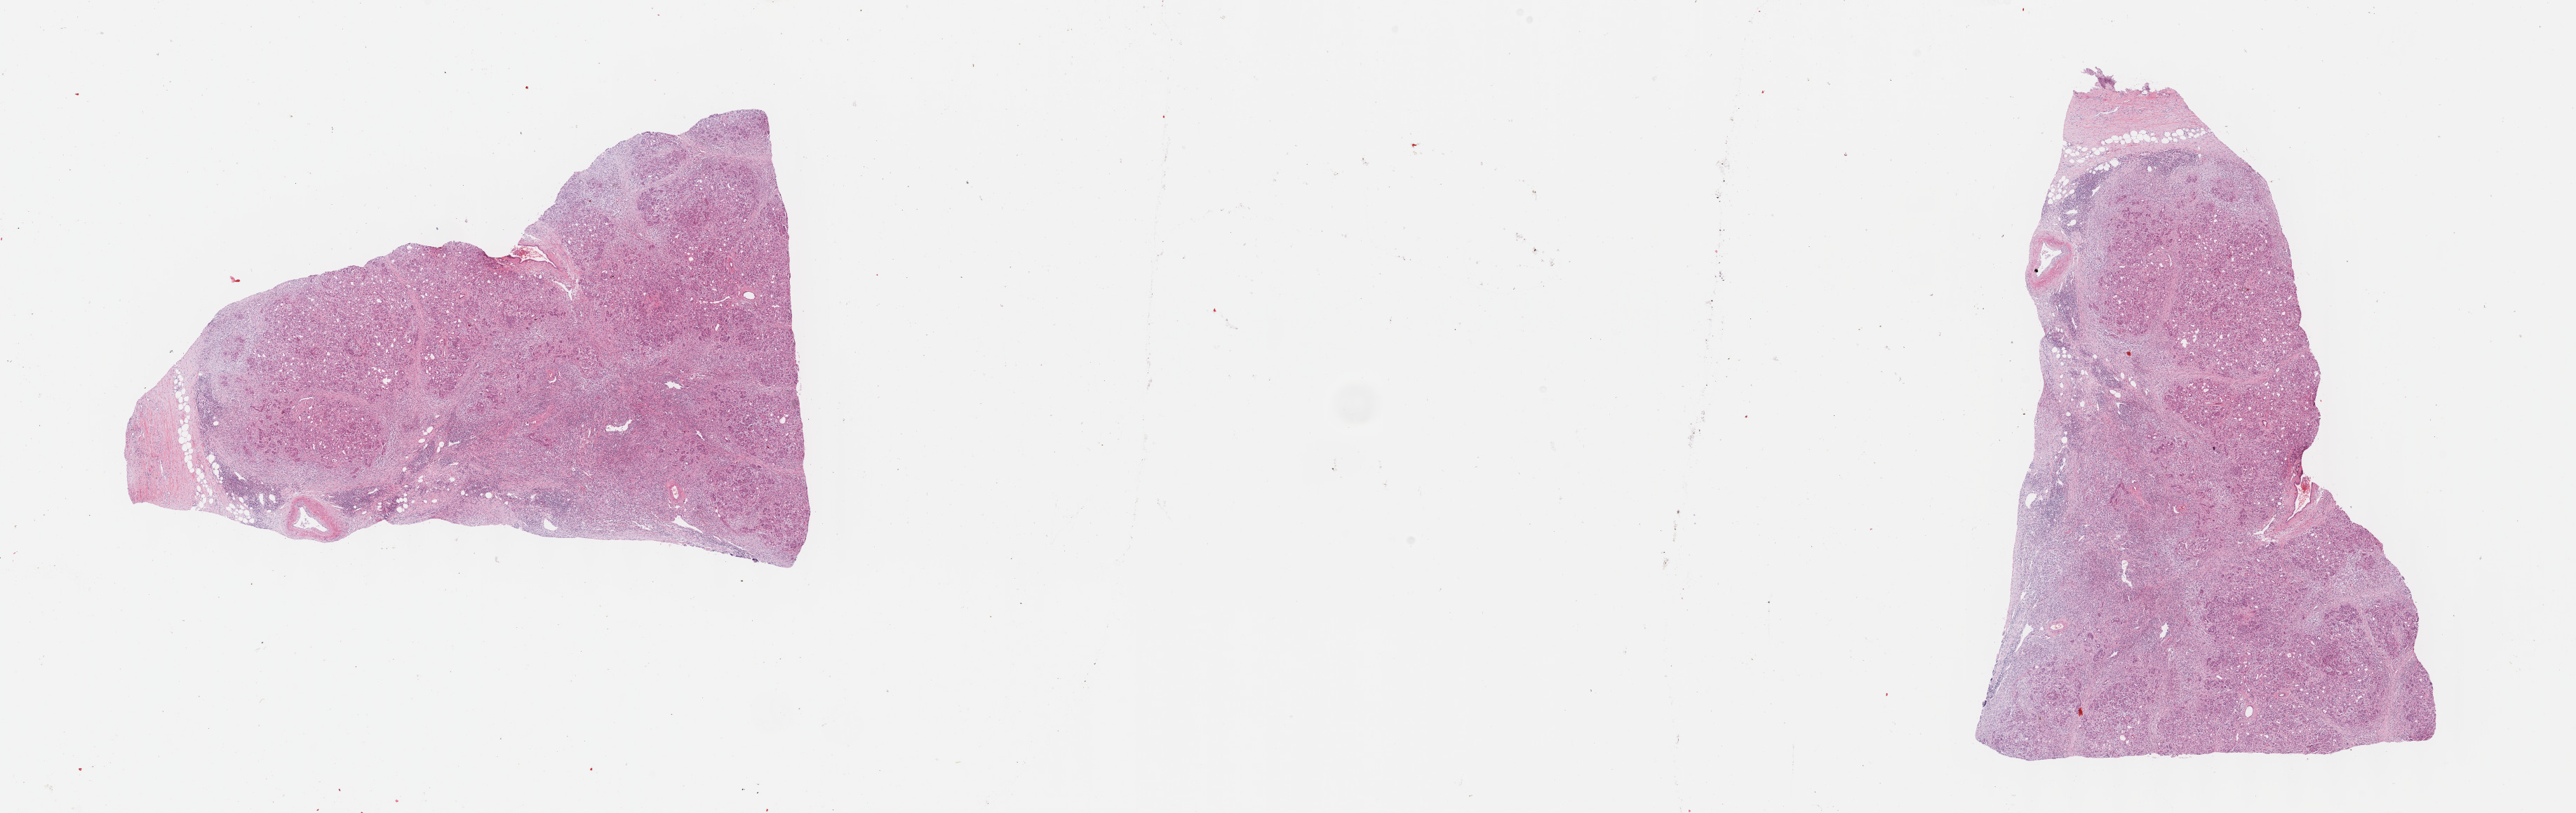
Whole-slide histology image, H&E-stained — low-resolution overview of the scanned area, about 29.7 x 9.4 mm; formalin-fixed paraffin-embedded (FFPE) diagnostic section; solid tissue normal (non-tumour tissue) sample from the pancreas. Patient: male, age at initial diagnosis 50 years.
This section: solid tissue normal (non-tumour) sample from the same patient. Patient diagnosis: Infiltrating duct carcinoma, NOS.